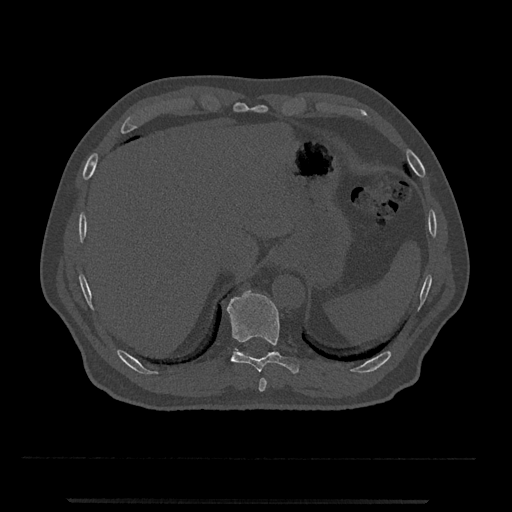
CT including the spine, one axial slice; reconstruction kernel Br40s/3; bone window (W 1800 / L 400 HU); 0.5 mm slice thickness; 512 × 512 image matrix, field of view 419 × 419 mm. Male patient, age 63 years. From the clinical record (not read from this slice): primary cancer: prostate.
Annotated regions visible in this slice (semi-automatic segmentation, software-assisted and operator-edited):
- T10 vertebra: bounding box [x1, y1, x2, y2] px = [226, 290, 300, 374]
- T11 vertebra: [235, 348, 243, 353]
- T9 vertebra: [259, 378, 267, 392]